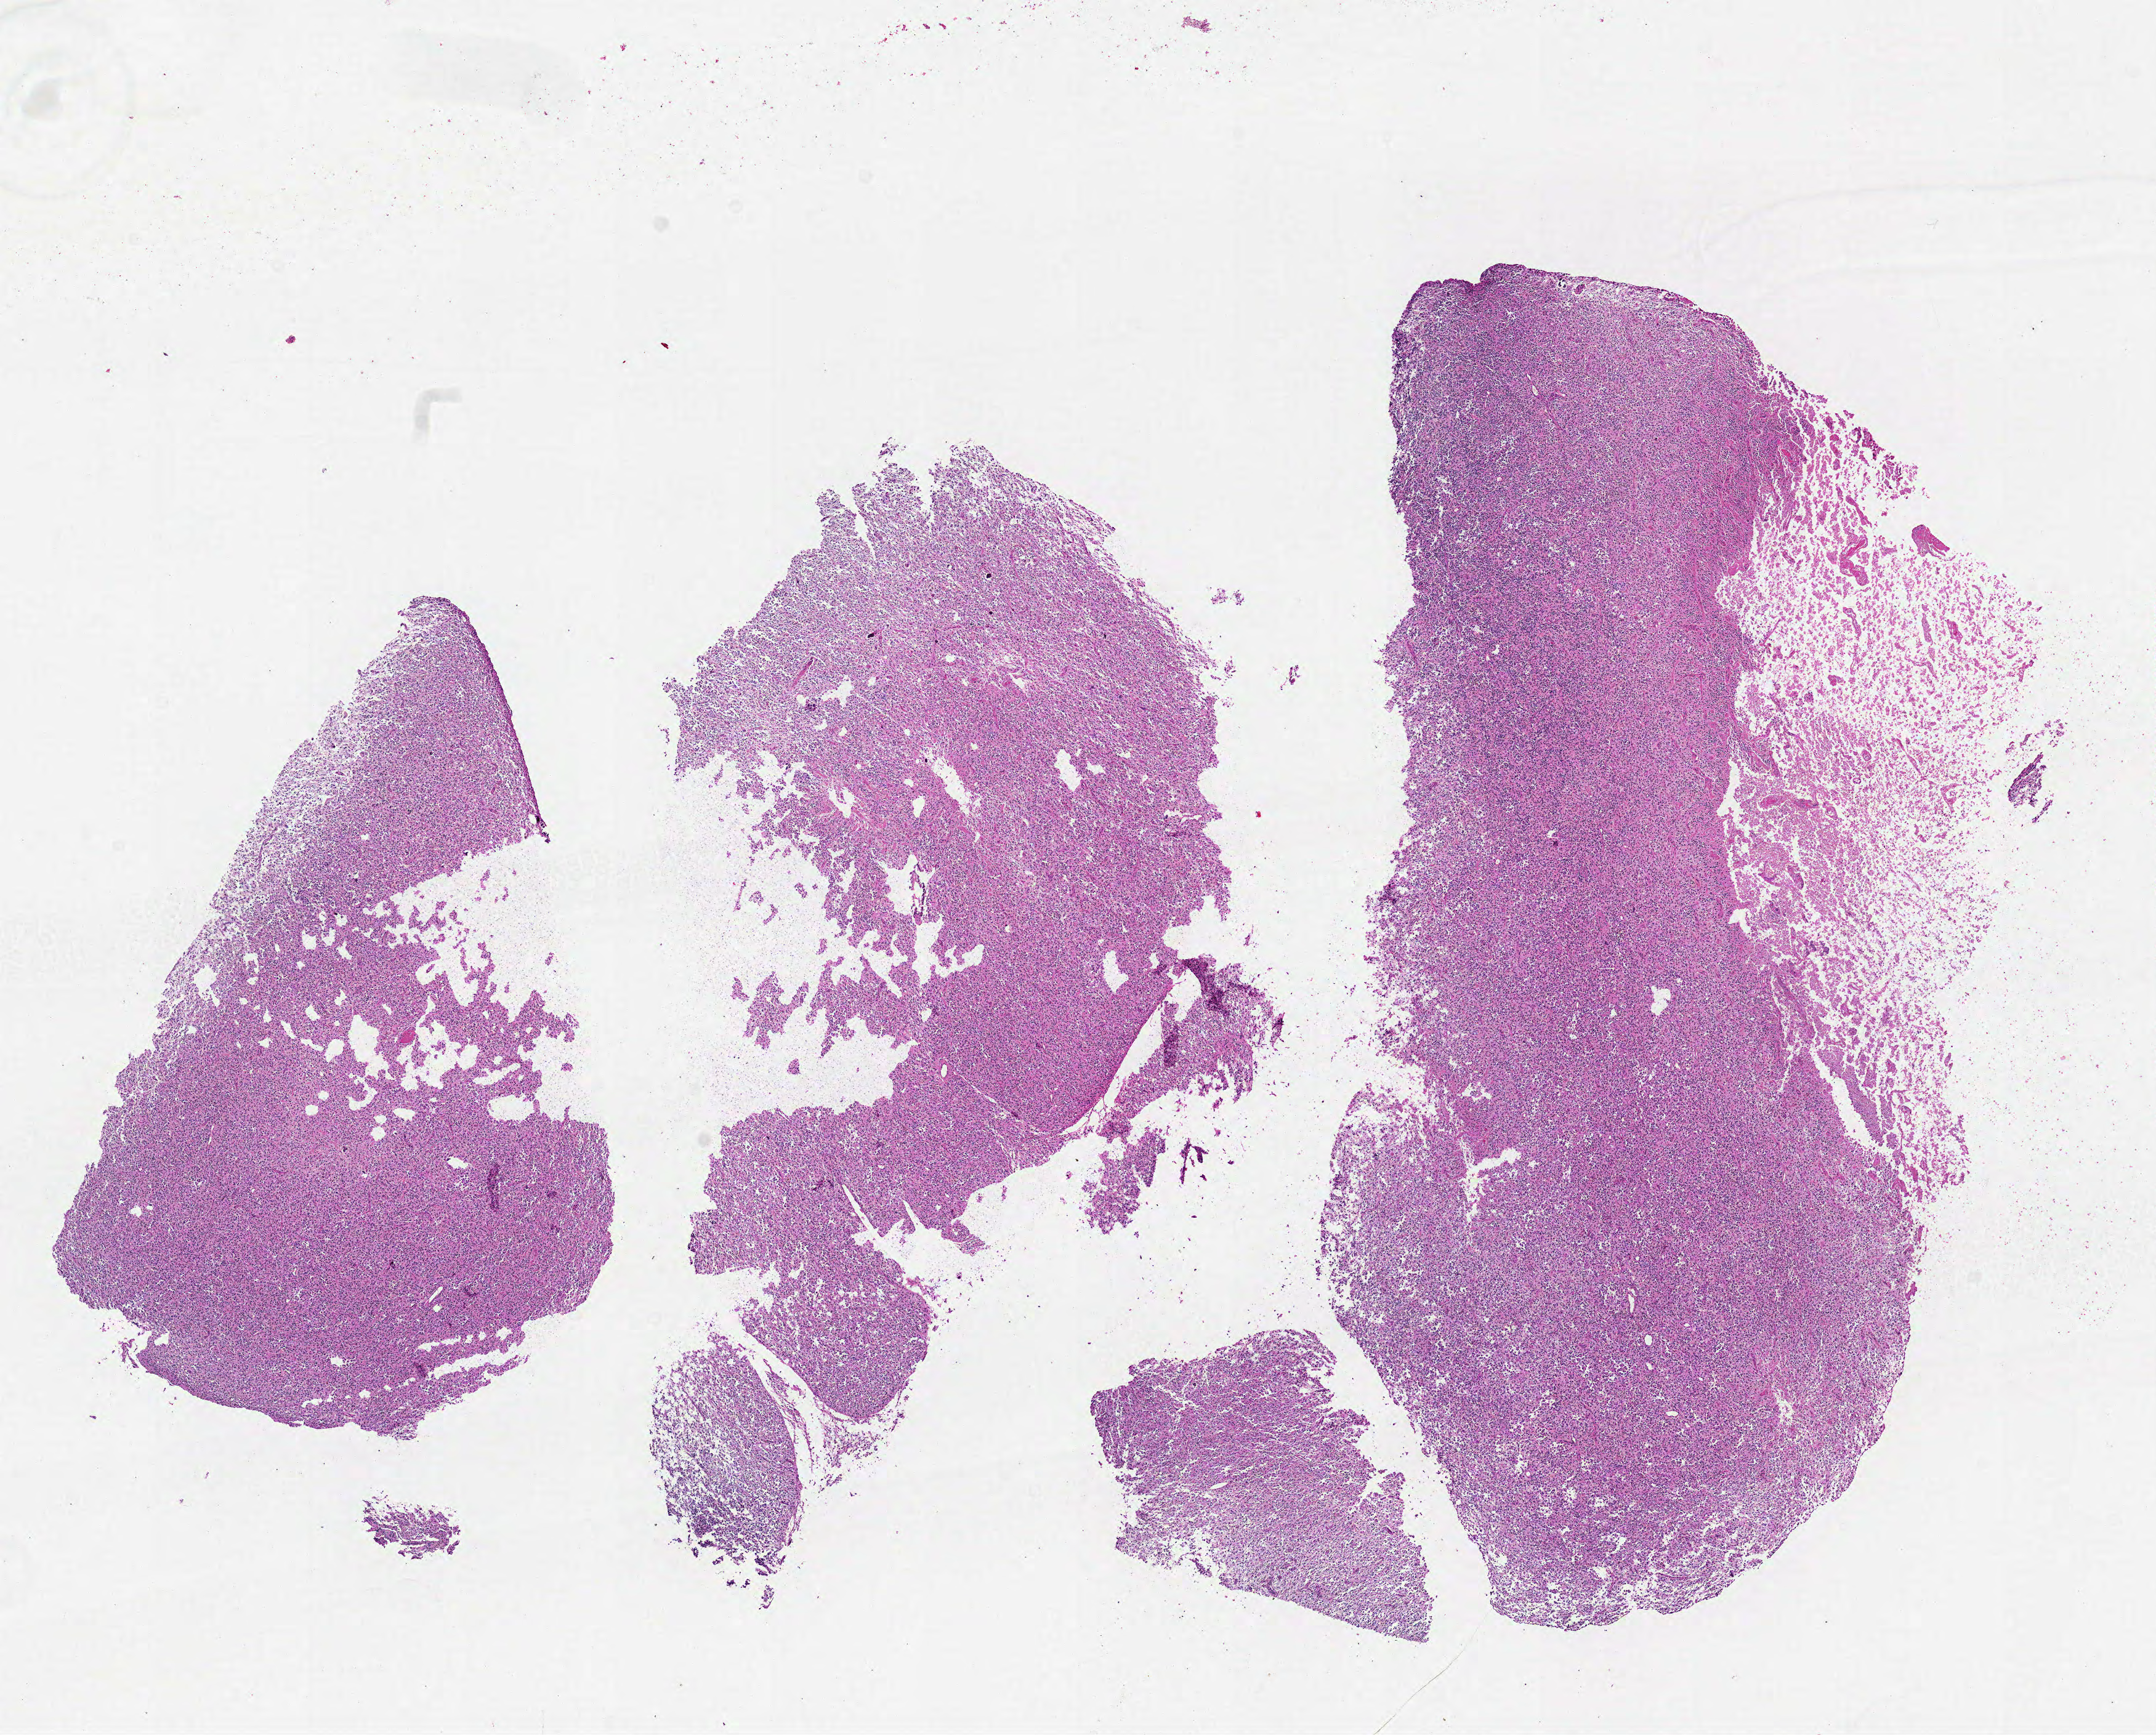
H&E-stained whole-slide image, a low-resolution overview of the entire scanned area, about 14.0 x 11.3 mm; formalin-fixed paraffin-embedded (FFPE) diagnostic section; primary tumour sample from the brain. Male patient; age at initial diagnosis 52 years.
* diagnosis: Glioblastoma